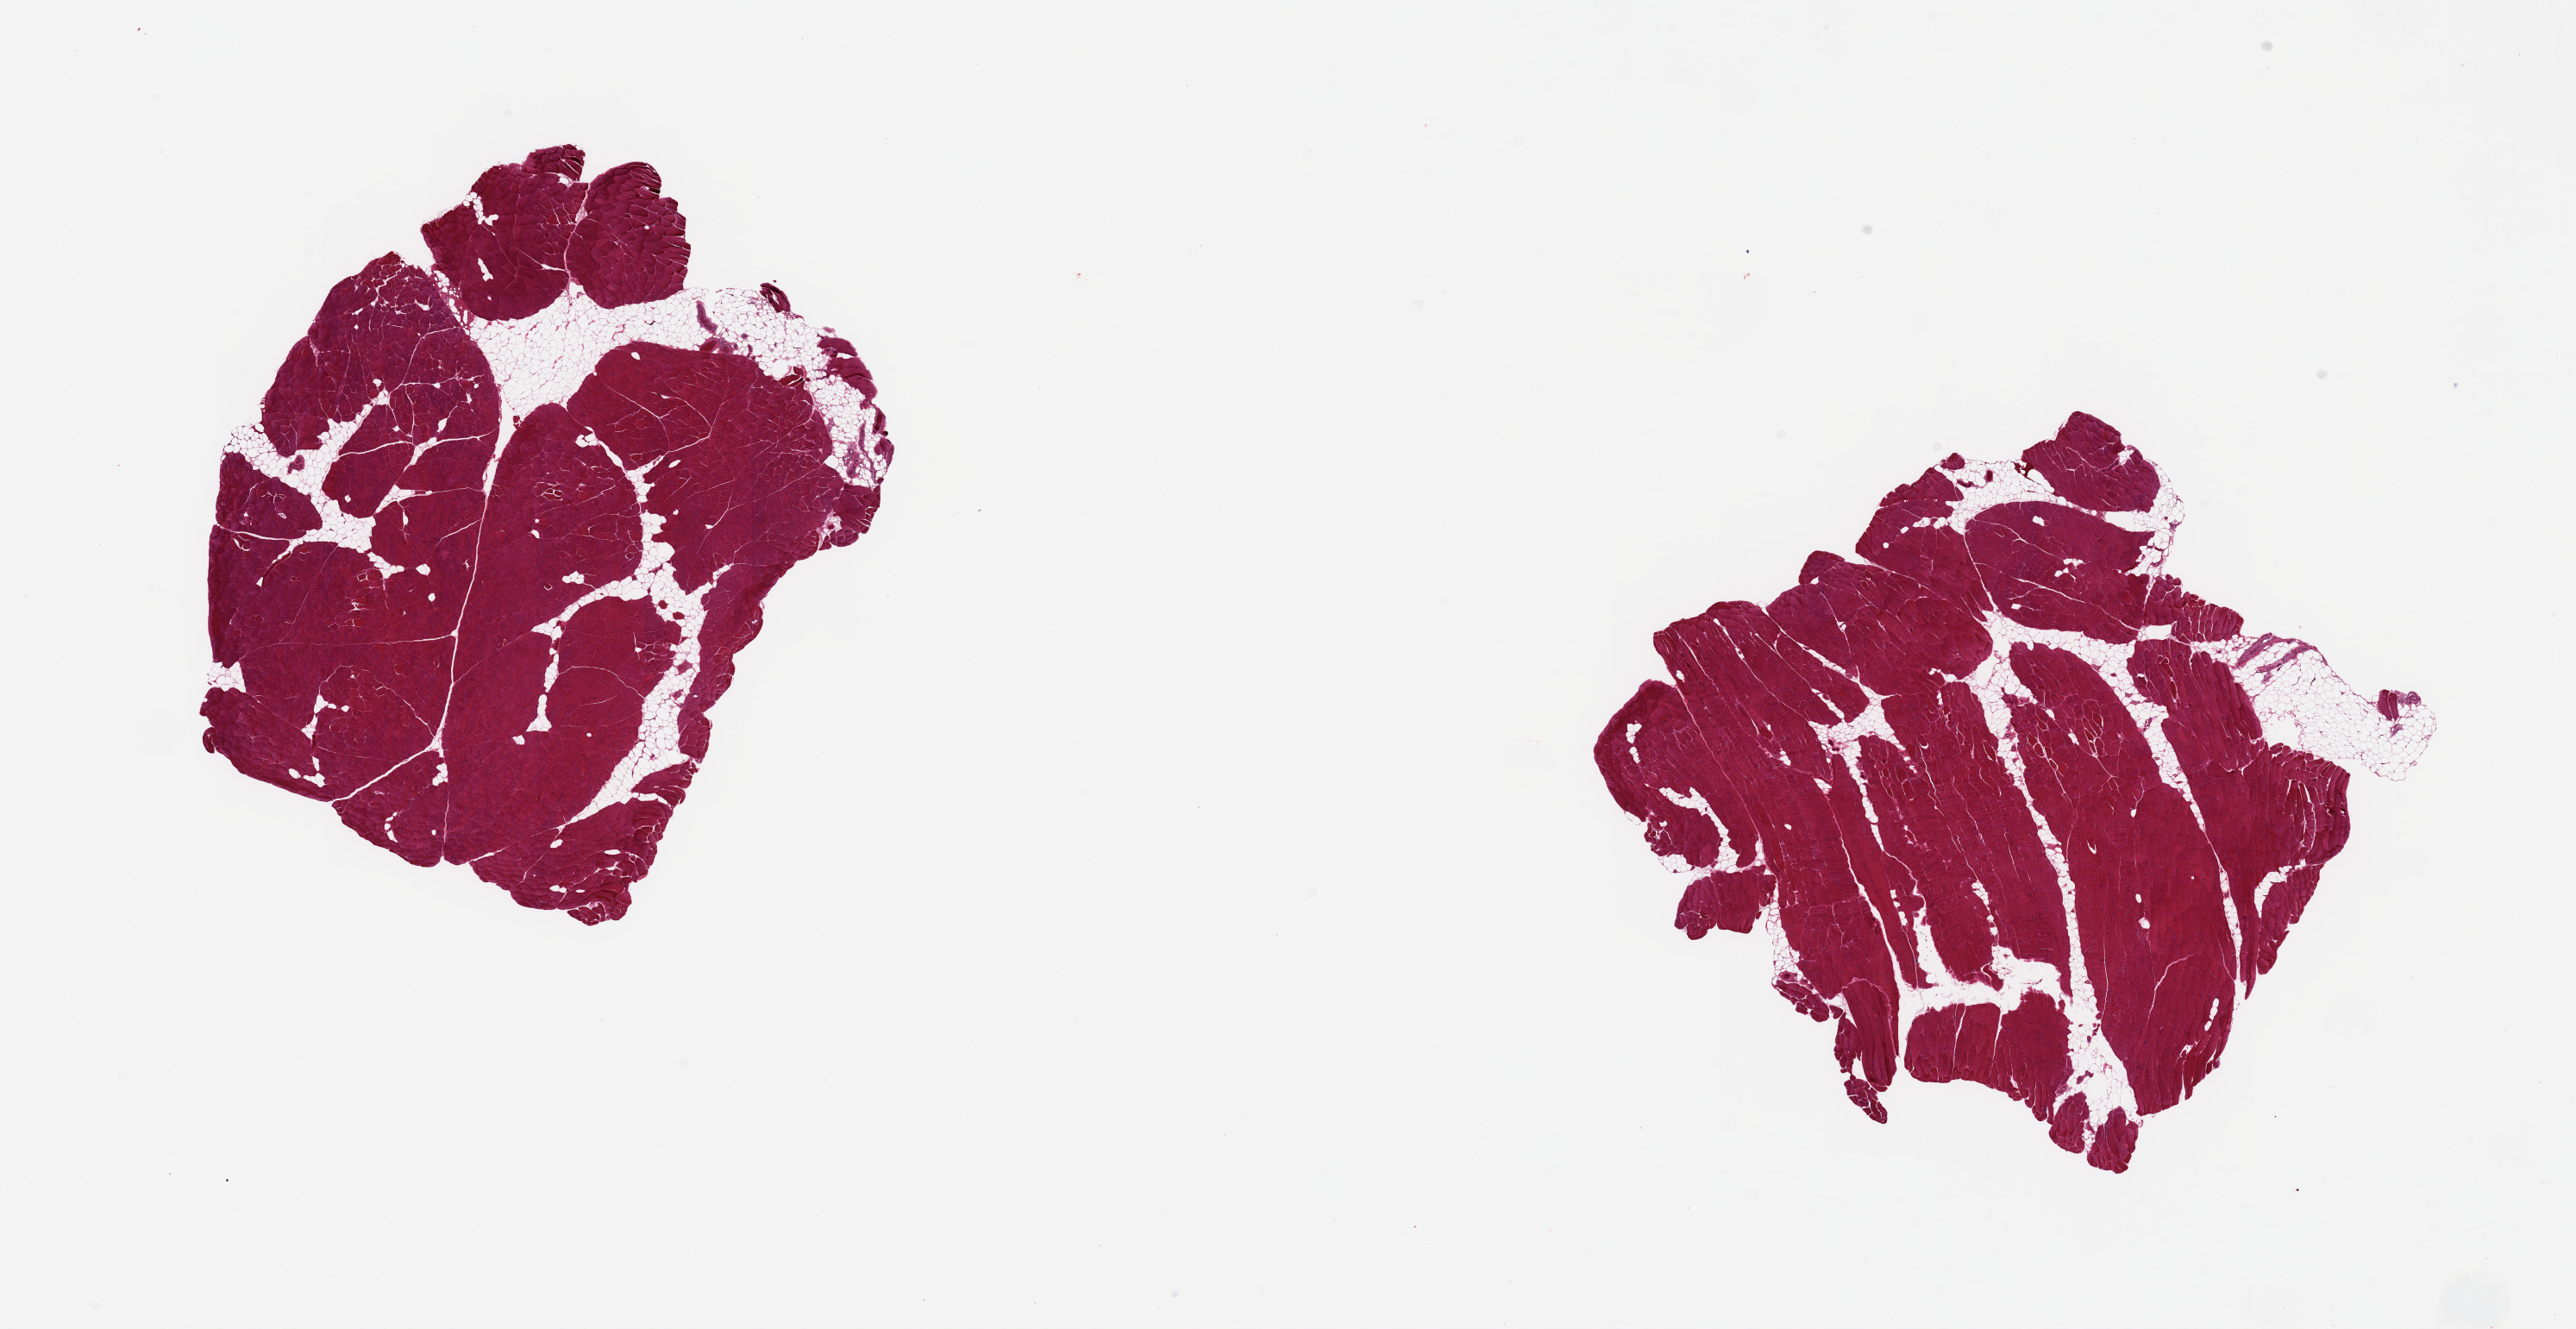
Haematoxylin and eosin whole-slide image, brightfield — a low-resolution overview of the entire scanned area, about 23.6 x 12.2 mm (acquisition: 20x scan); PAXgene-fixed, paraffin-embedded tissue; section of skeletal muscle (target tissue); tissue donor sample. Donor: female.
- review note (as recorded): 2 pieces; 15% internal fat